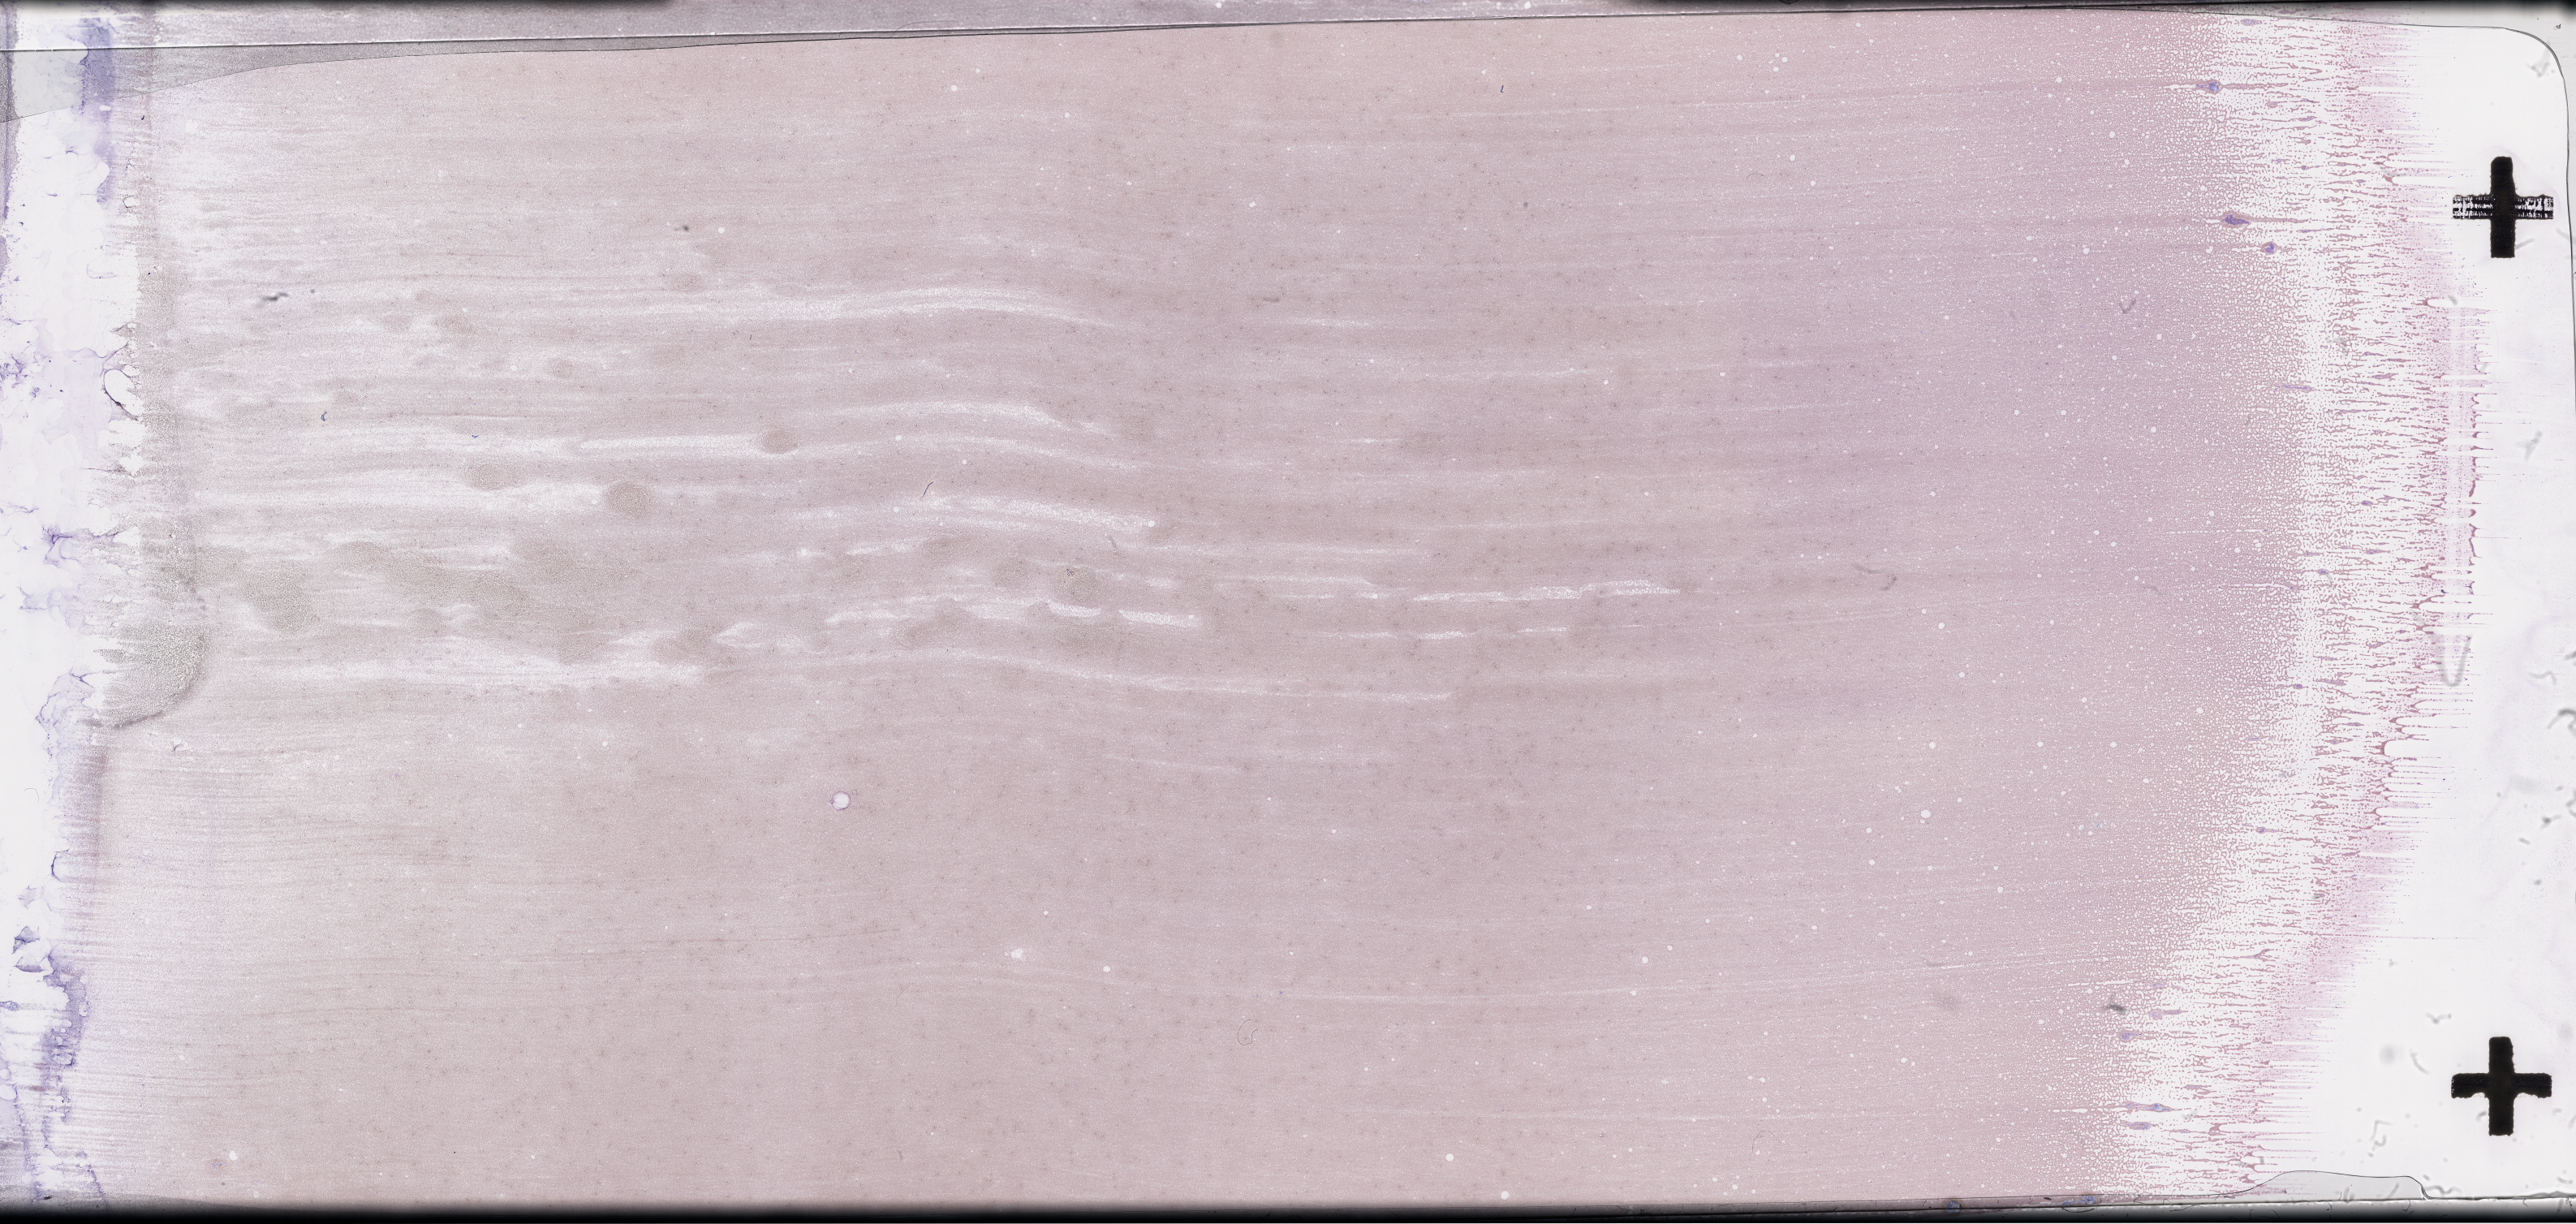
Wright-Giemsa-stained whole blood smear, whole-slide image — low-resolution overview of the scanned area, about 51.3 x 24.4 mm. Male patient.
Patient diagnosis: Plasma Cell Myeloma.